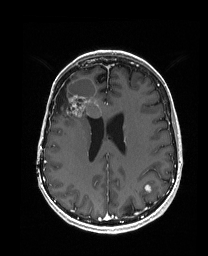
Brain MRI from a brain-tumour surgery series, one axial slice; slice 71 of 192 in the series (ordered by position); T1-weighted post-contrast; 1 mm slice thickness; 208 × 256 image matrix. From the clinical record (not read from this slice): histopathology: Metastatic Carcinoma from Breast primary; tumour location: Right Frontal.
Structures marked on this image (outlined manually by an expert reader):
- previous resection cavity: bounding box <53,79,70,113> (left, top, right, bottom; pixels)
- tumour: <55,77,104,128>